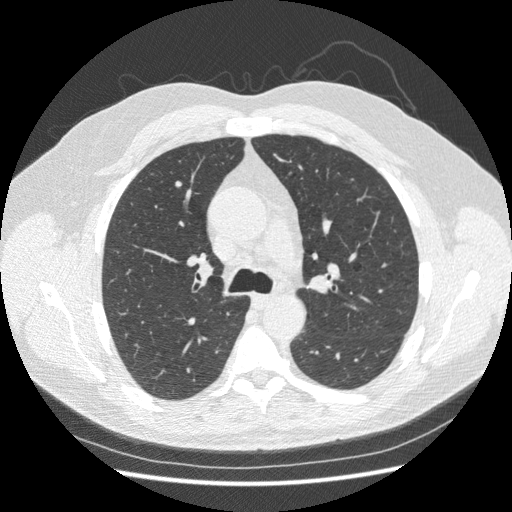
Low-dose screening chest CT, one axial slice; position 159 of 250 along the scan axis; reconstruction kernel STANDARD; 120 kVp; lung window (W 1500 / L -600 HU); 512 × 512 image matrix.
Annotated regions visible in this slice (outlined manually by an expert reader):
- lesion 1 (tumor, upper lobe of right lung): bounding box <174,180,183,188> (left, top, right, bottom; pixels)